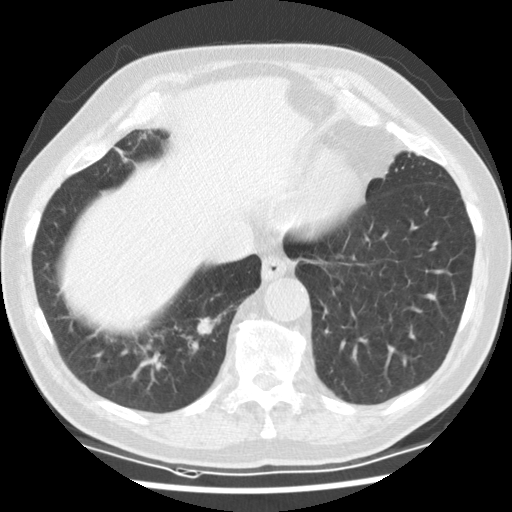
Low-dose screening chest CT, one axial slice. Slice 25 of 135 in the series (ordered by position). Reconstruction kernel STANDARD. 120 kVp. Lung window (W 1500 / L -600 HU). 2.5 mm slice thickness. 512 × 512 image matrix, field of view 340 × 340 mm.
Structures marked on this image (expert manual segmentation):
- lesion 2 (nodule, upper lobe of right lung): bounding box (x1, y1, x2, y2) in pixels: (197, 312, 226, 335)